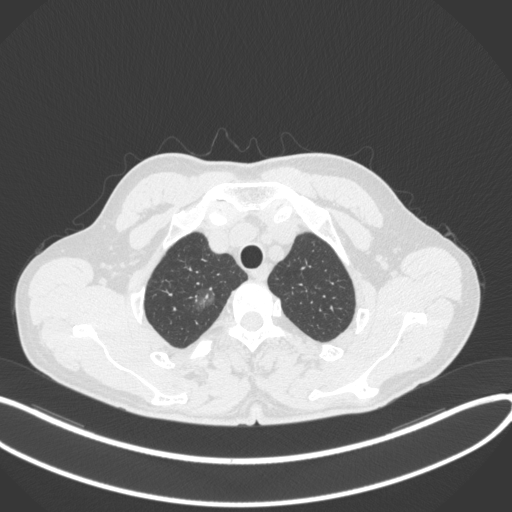
Chest CT, one axial slice. Slice 329 of 407 in the series (ordered by position). Reconstruction kernel B31f. 120 kVp. Lung window (W 1500 / L -600 HU). 1 mm slice thickness. 512 × 512 image matrix, field of view 400 × 400 mm. Male patient, age 58 years. From the clinical record (not read from this slice): clinical TNM (as recorded): T1c N0 M0.
Structures marked on this image (rectangle marked by the reading radiologist):
- lung tumour (recorded histology: adenocarcinoma): bounding box <186,278,221,316> (left, top, right, bottom; pixels)